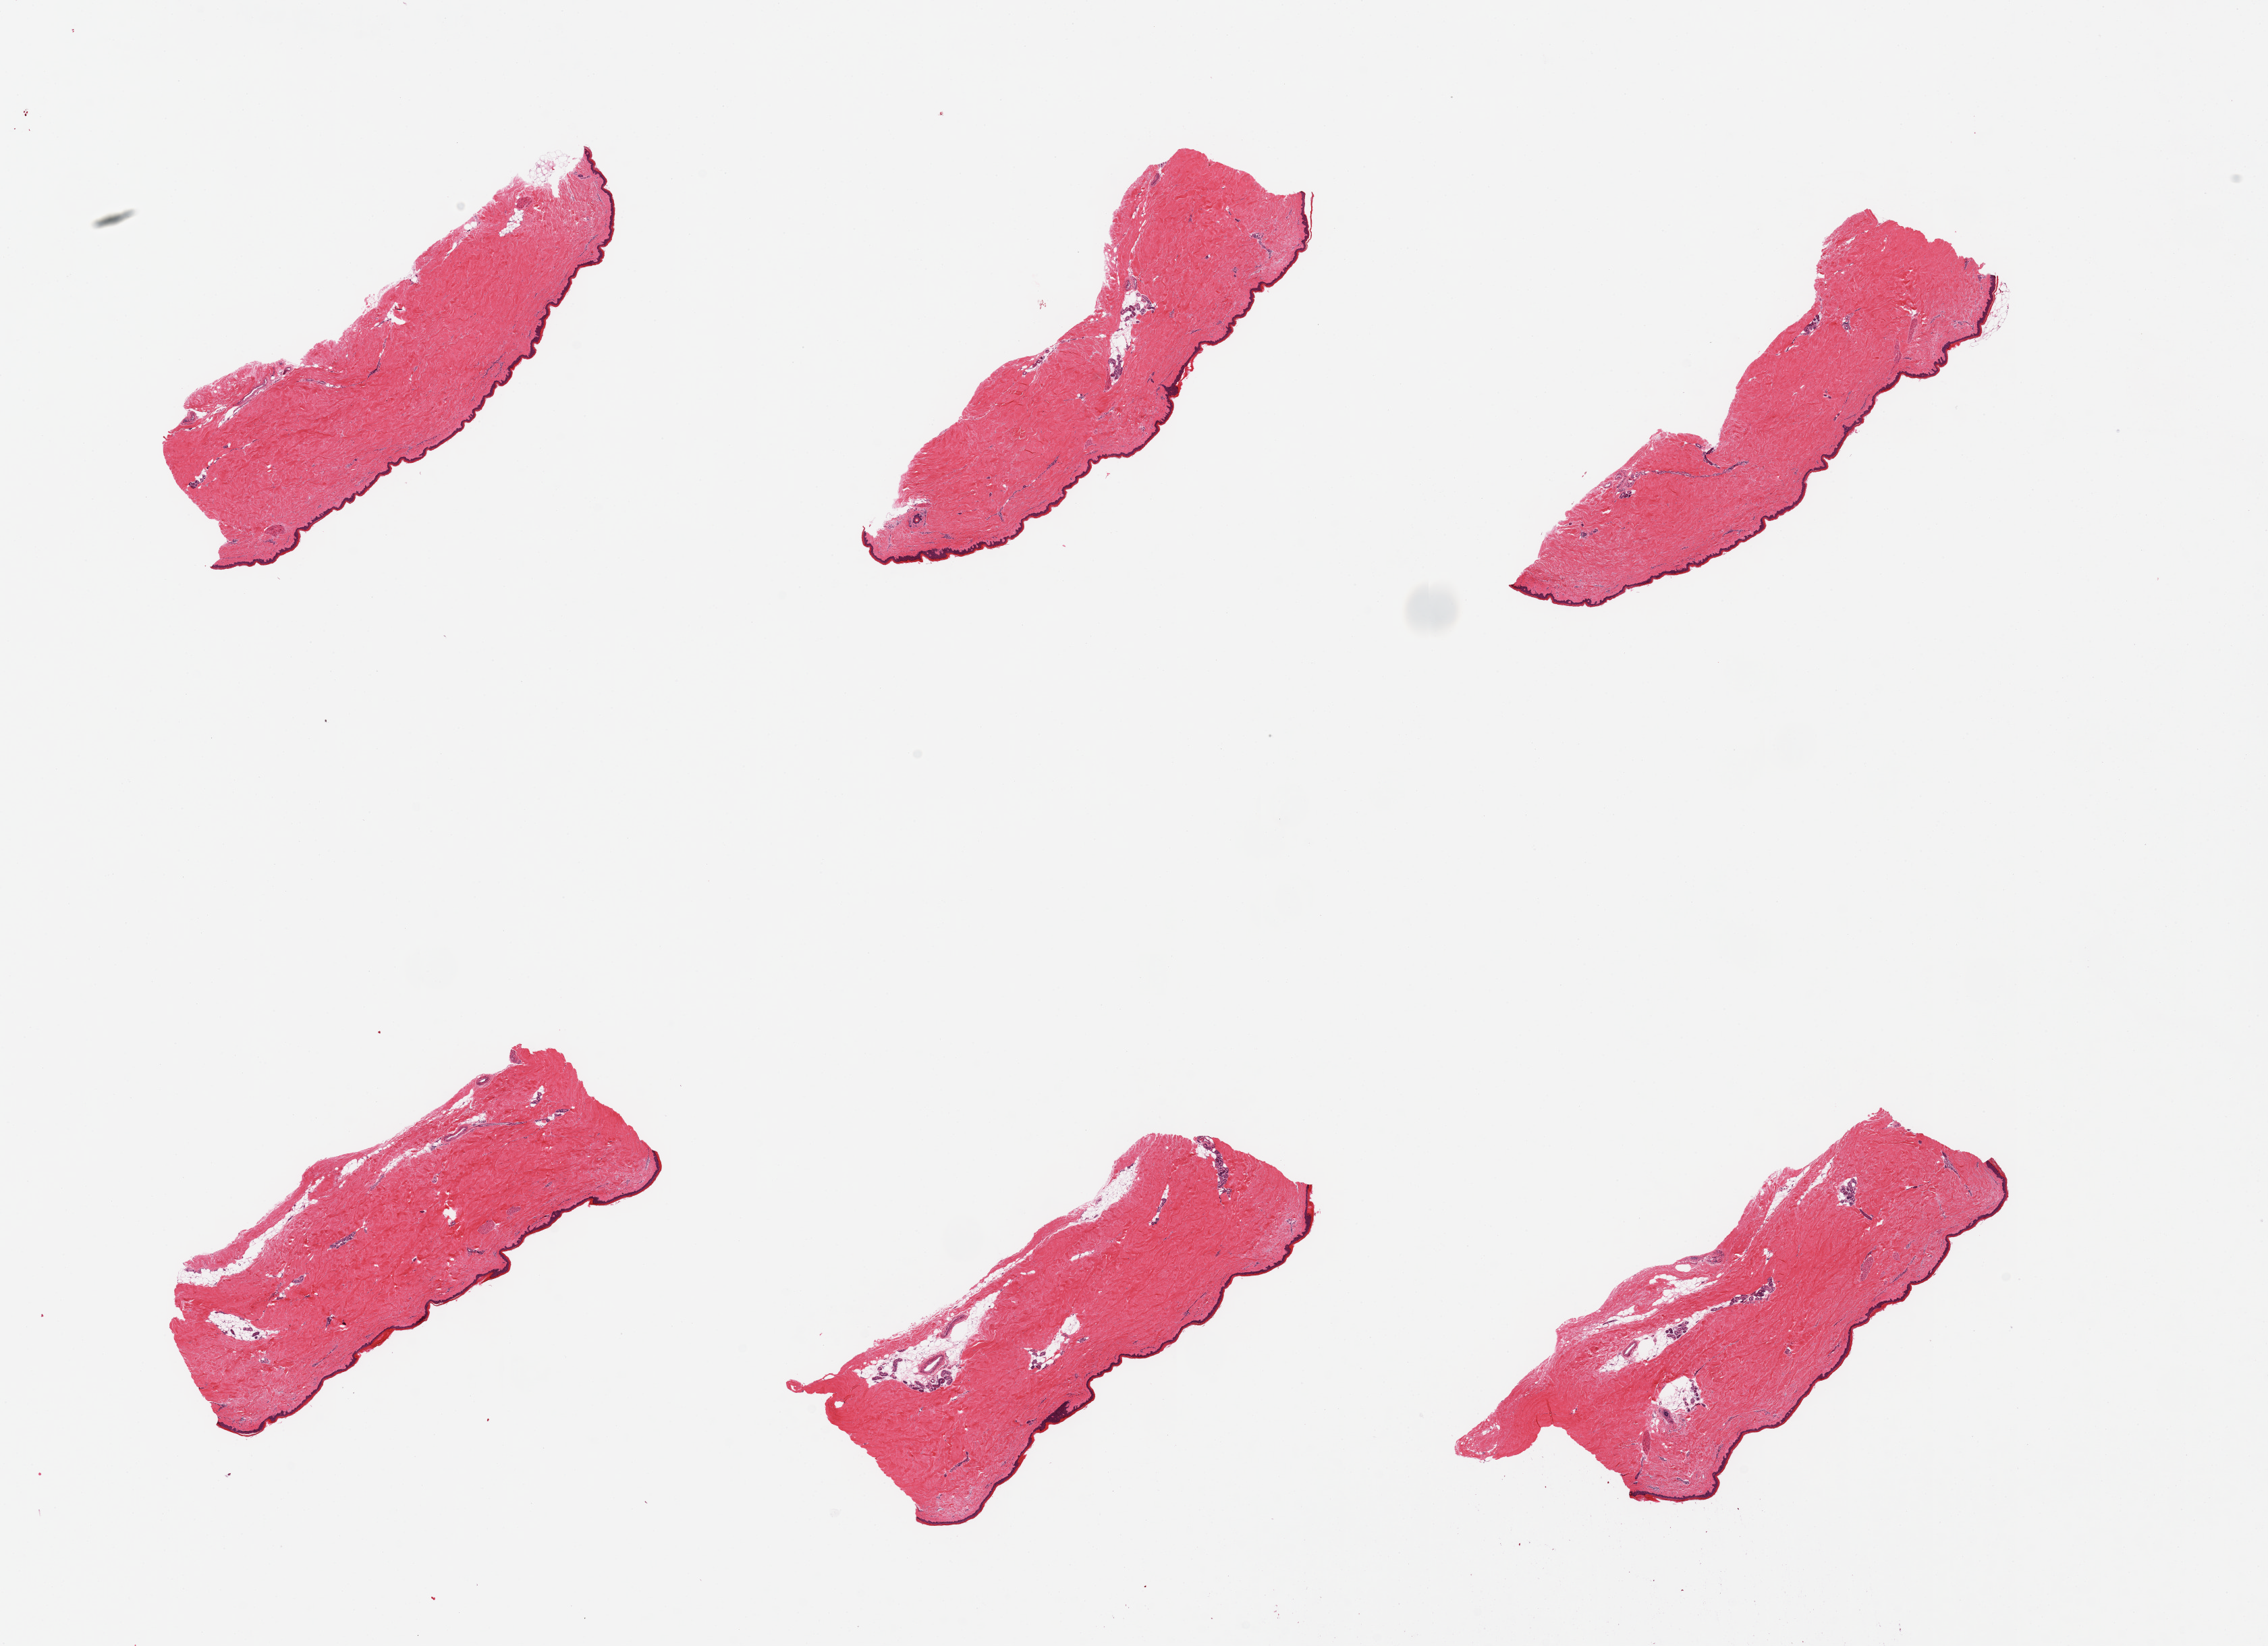
Whole-slide image, hematoxylin and eosin (H&E) stain, brightfield, a low-resolution overview of the entire scanned area, about 26.6 x 19.3 mm, PAXgene-fixed, paraffin-embedded tissue, target tissue: skin of lower leg, donor tissue sample. Female donor.
Review note (as recorded): 6 pieces, minimal dermal fat, squamous epithelium is ~30 microns.